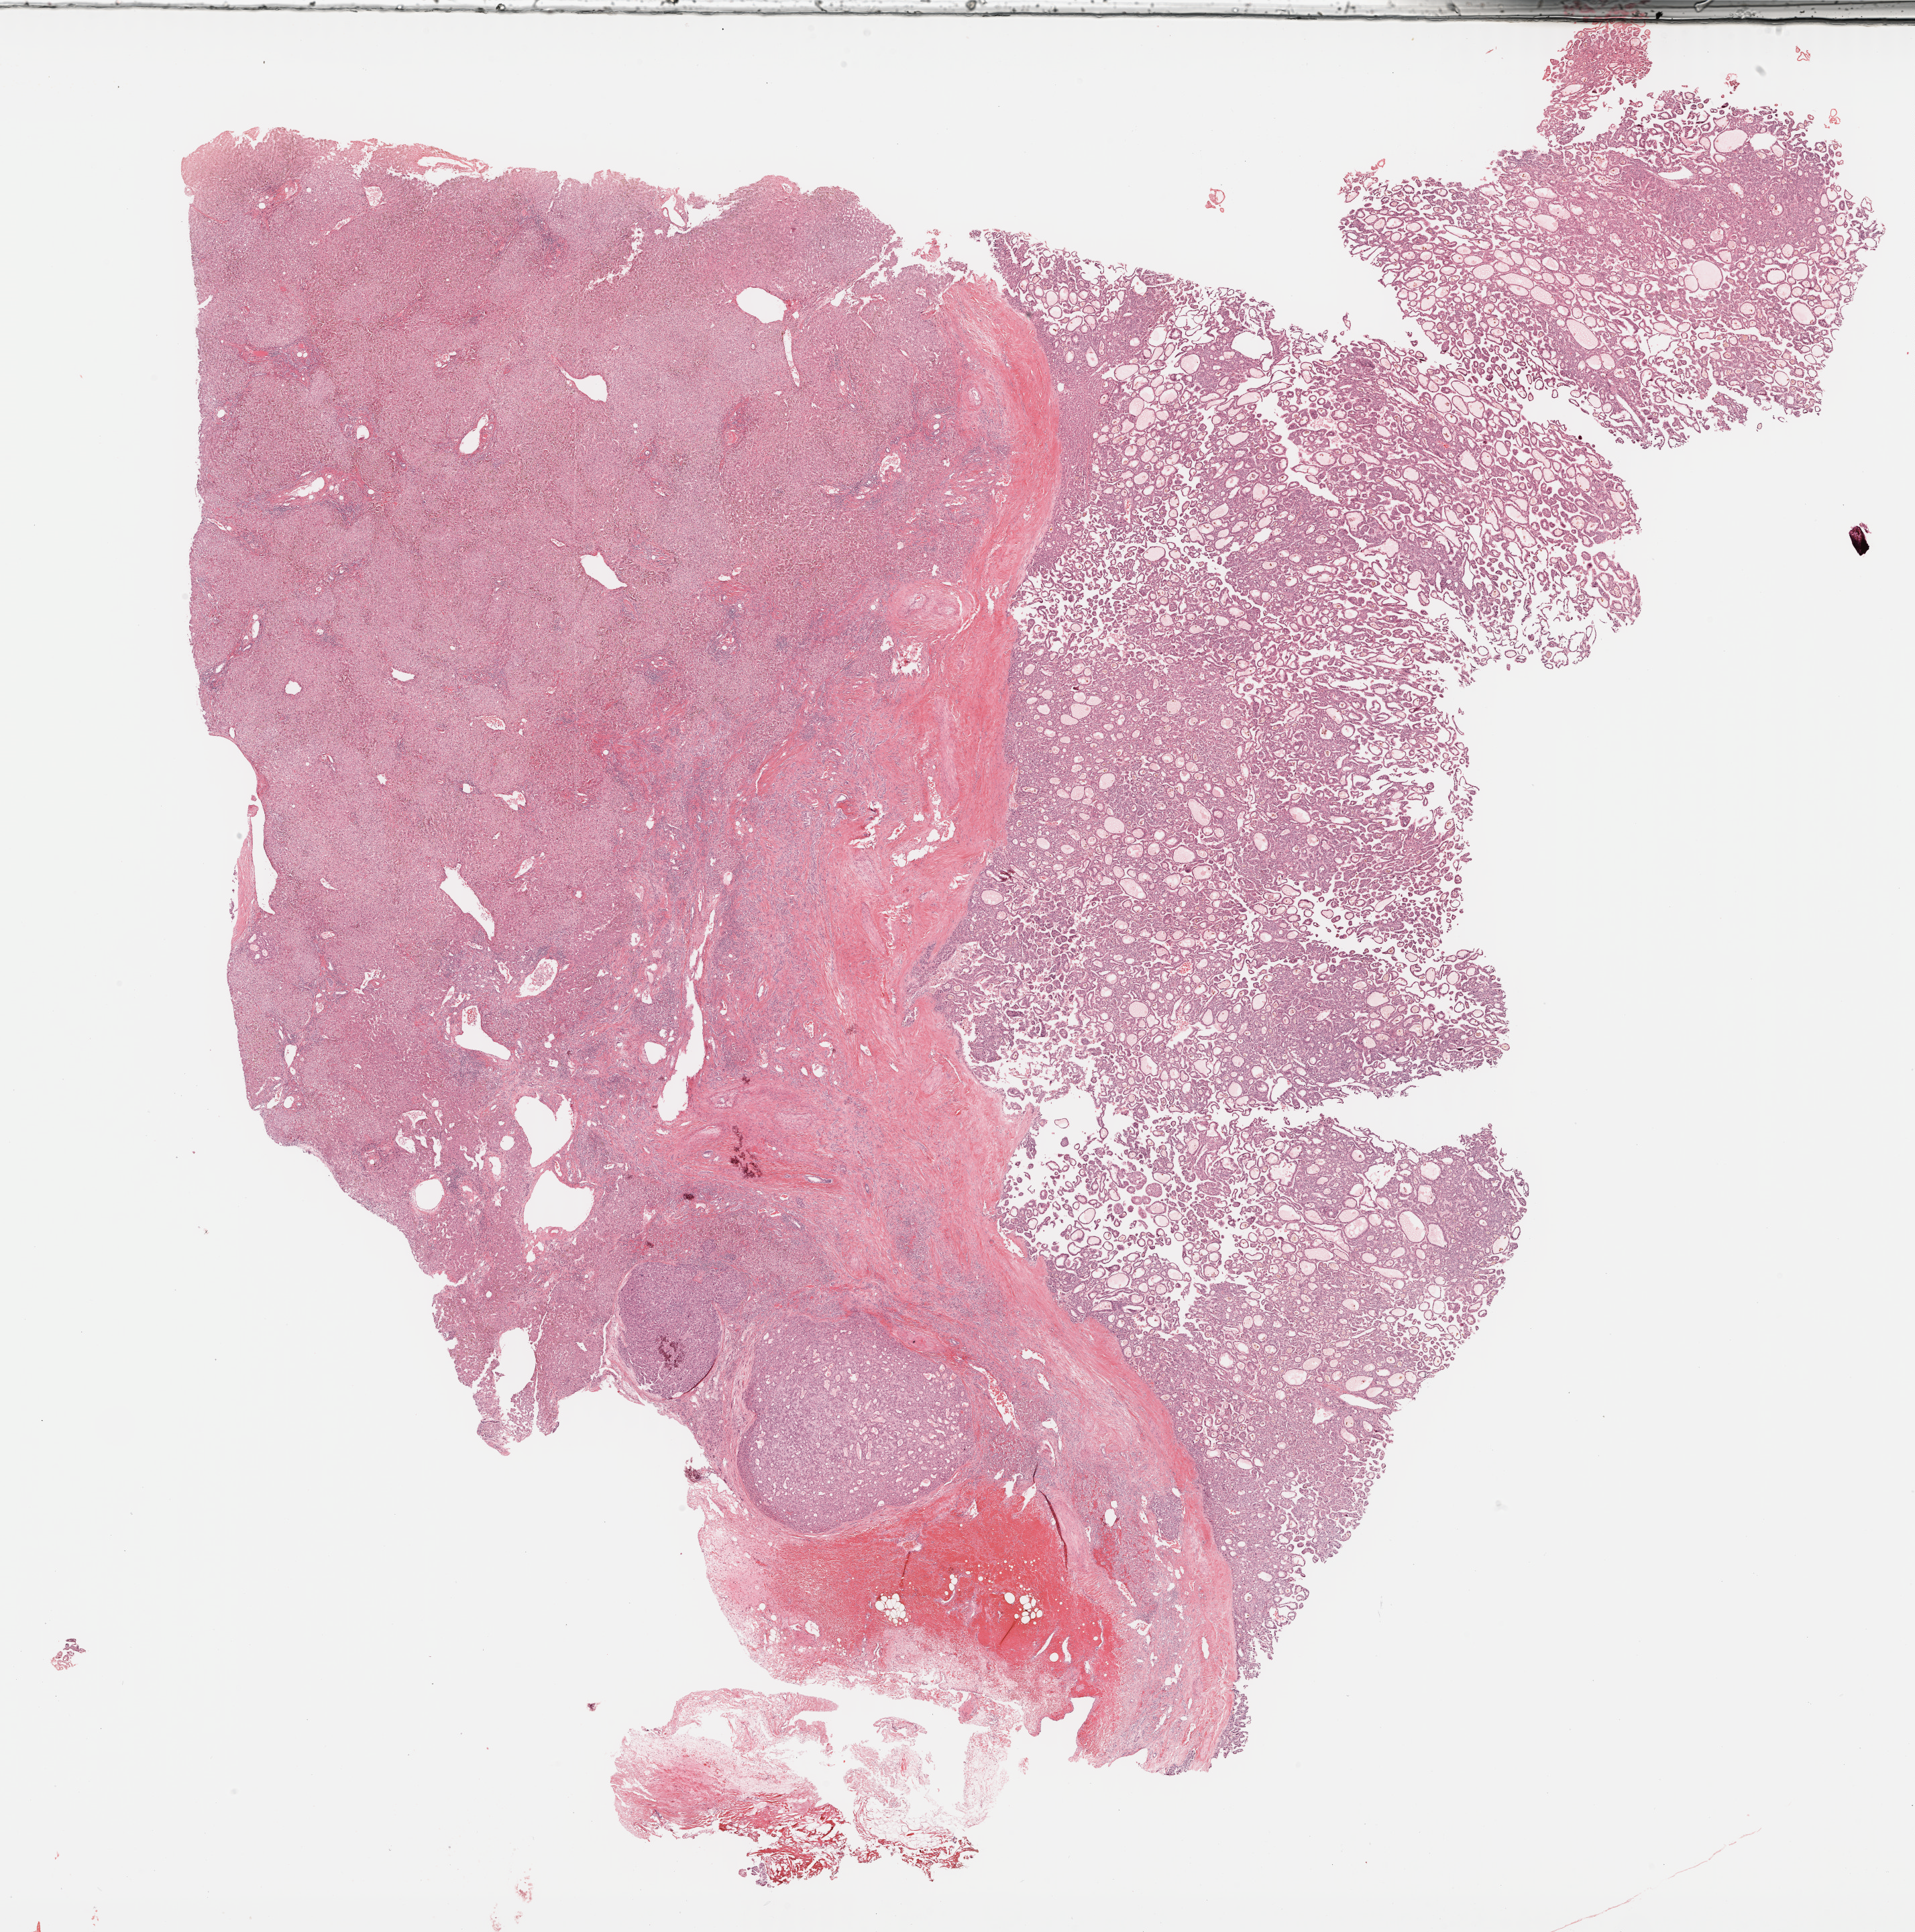
Digitized H&E-stained tissue section (whole slide) — low-resolution overview of the scanned area, about 23.1 x 23.3 mm (from a 40x scan). FFPE section. Sample: primary tumour, liver. Patient: male, age at initial diagnosis 75 years. Histologic grade: G2 (moderately differentiated).
Pathologic diagnosis: Hepatocellular carcinoma, NOS. AJCC pathologic stage: II. TNM: T2 N0 M0.